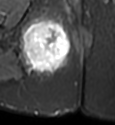
MRI of an extremity soft-tissue mass, one axial slice; position 26 of 49 along the scan axis; STIR; MR volume resampled by the dataset authors to the PET/CT grid (not the native acquisition matrix); 3.27 mm slice thickness; 115 × 125 image matrix. Female patient. From the clinical record (not read from this slice): histological type: epithelioid sarcoma; grade: intermediate; site of the primary tumour: right buttock.
Outlined on this slice (expert contour drawn on MRI and transferred to this co-registered scan by the dataset authors):
- gross tumour volume including surrounding oedema: bounding box [x1, y1, x2, y2] px = [19, 14, 71, 76]
- gross tumour volume (mass): [24, 23, 69, 69]